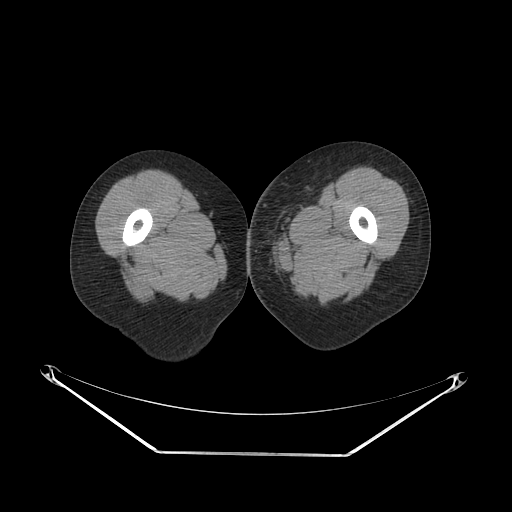
CT of an extremity soft-tissue mass (from a PET/CT study), one axial slice; reconstruction kernel SOFT; 140 kVp; soft-tissue window (W 400 / L 40 HU); 3.75 mm slice thickness; 512 × 512 image matrix, field of view 500 × 500 mm. Female patient. Case-level facts recorded for this patient, not image findings: histological type: leiomyosarcoma; grade: high; site of the primary tumour: groin.
Outlined on this slice (expert contour drawn on MRI and transferred to this co-registered scan by the dataset authors):
- gross tumour volume including surrounding oedema: bounding box (x1, y1, x2, y2) in pixels: (246, 210, 286, 250)